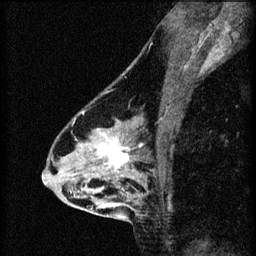
Breast MRI (dynamic contrast-enhanced), one sagittal slice. Slice 41 of 60 in the series (ordered by position). 3 images stored at this slice position (order not interpretable as contrast timing). 1.5 T. TE 4.2 ms, TR 8.2 ms. 256 × 256 image matrix, field of view 180 × 180 mm. Patient: female, 46 years.
Annotated regions visible in this slice (semi-automatically segmented with operator editing):
- analysis volume of interest (the breast-tissue region the enhancement analysis was run in; not a lesion): bounding box <55,114,148,209> (left, top, right, bottom; pixels)
- tumour enhancement mask (voxels above the 70 % enhancement threshold inside the analysis volume of interest): <75,114,143,169>